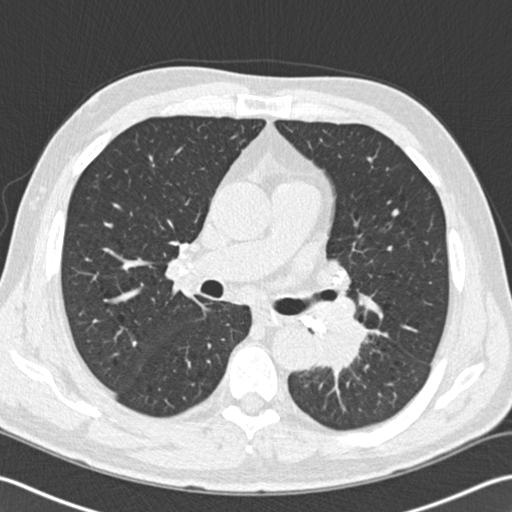
Low-dose screening chest CT, one axial slice. Slice 102 of 170 in the series (ordered by position). Reconstruction kernel B30f. 120 kVp. Lung window (W 1500 / L -600 HU). 2 mm slice thickness. 512 × 512 image matrix, field of view 350 × 350 mm.
Annotated regions visible in this slice (outlined manually by an expert reader):
- lesion 1 (tumor, lower lobe of left lung): box from (x=318, y=317) to (x=367, y=369) px